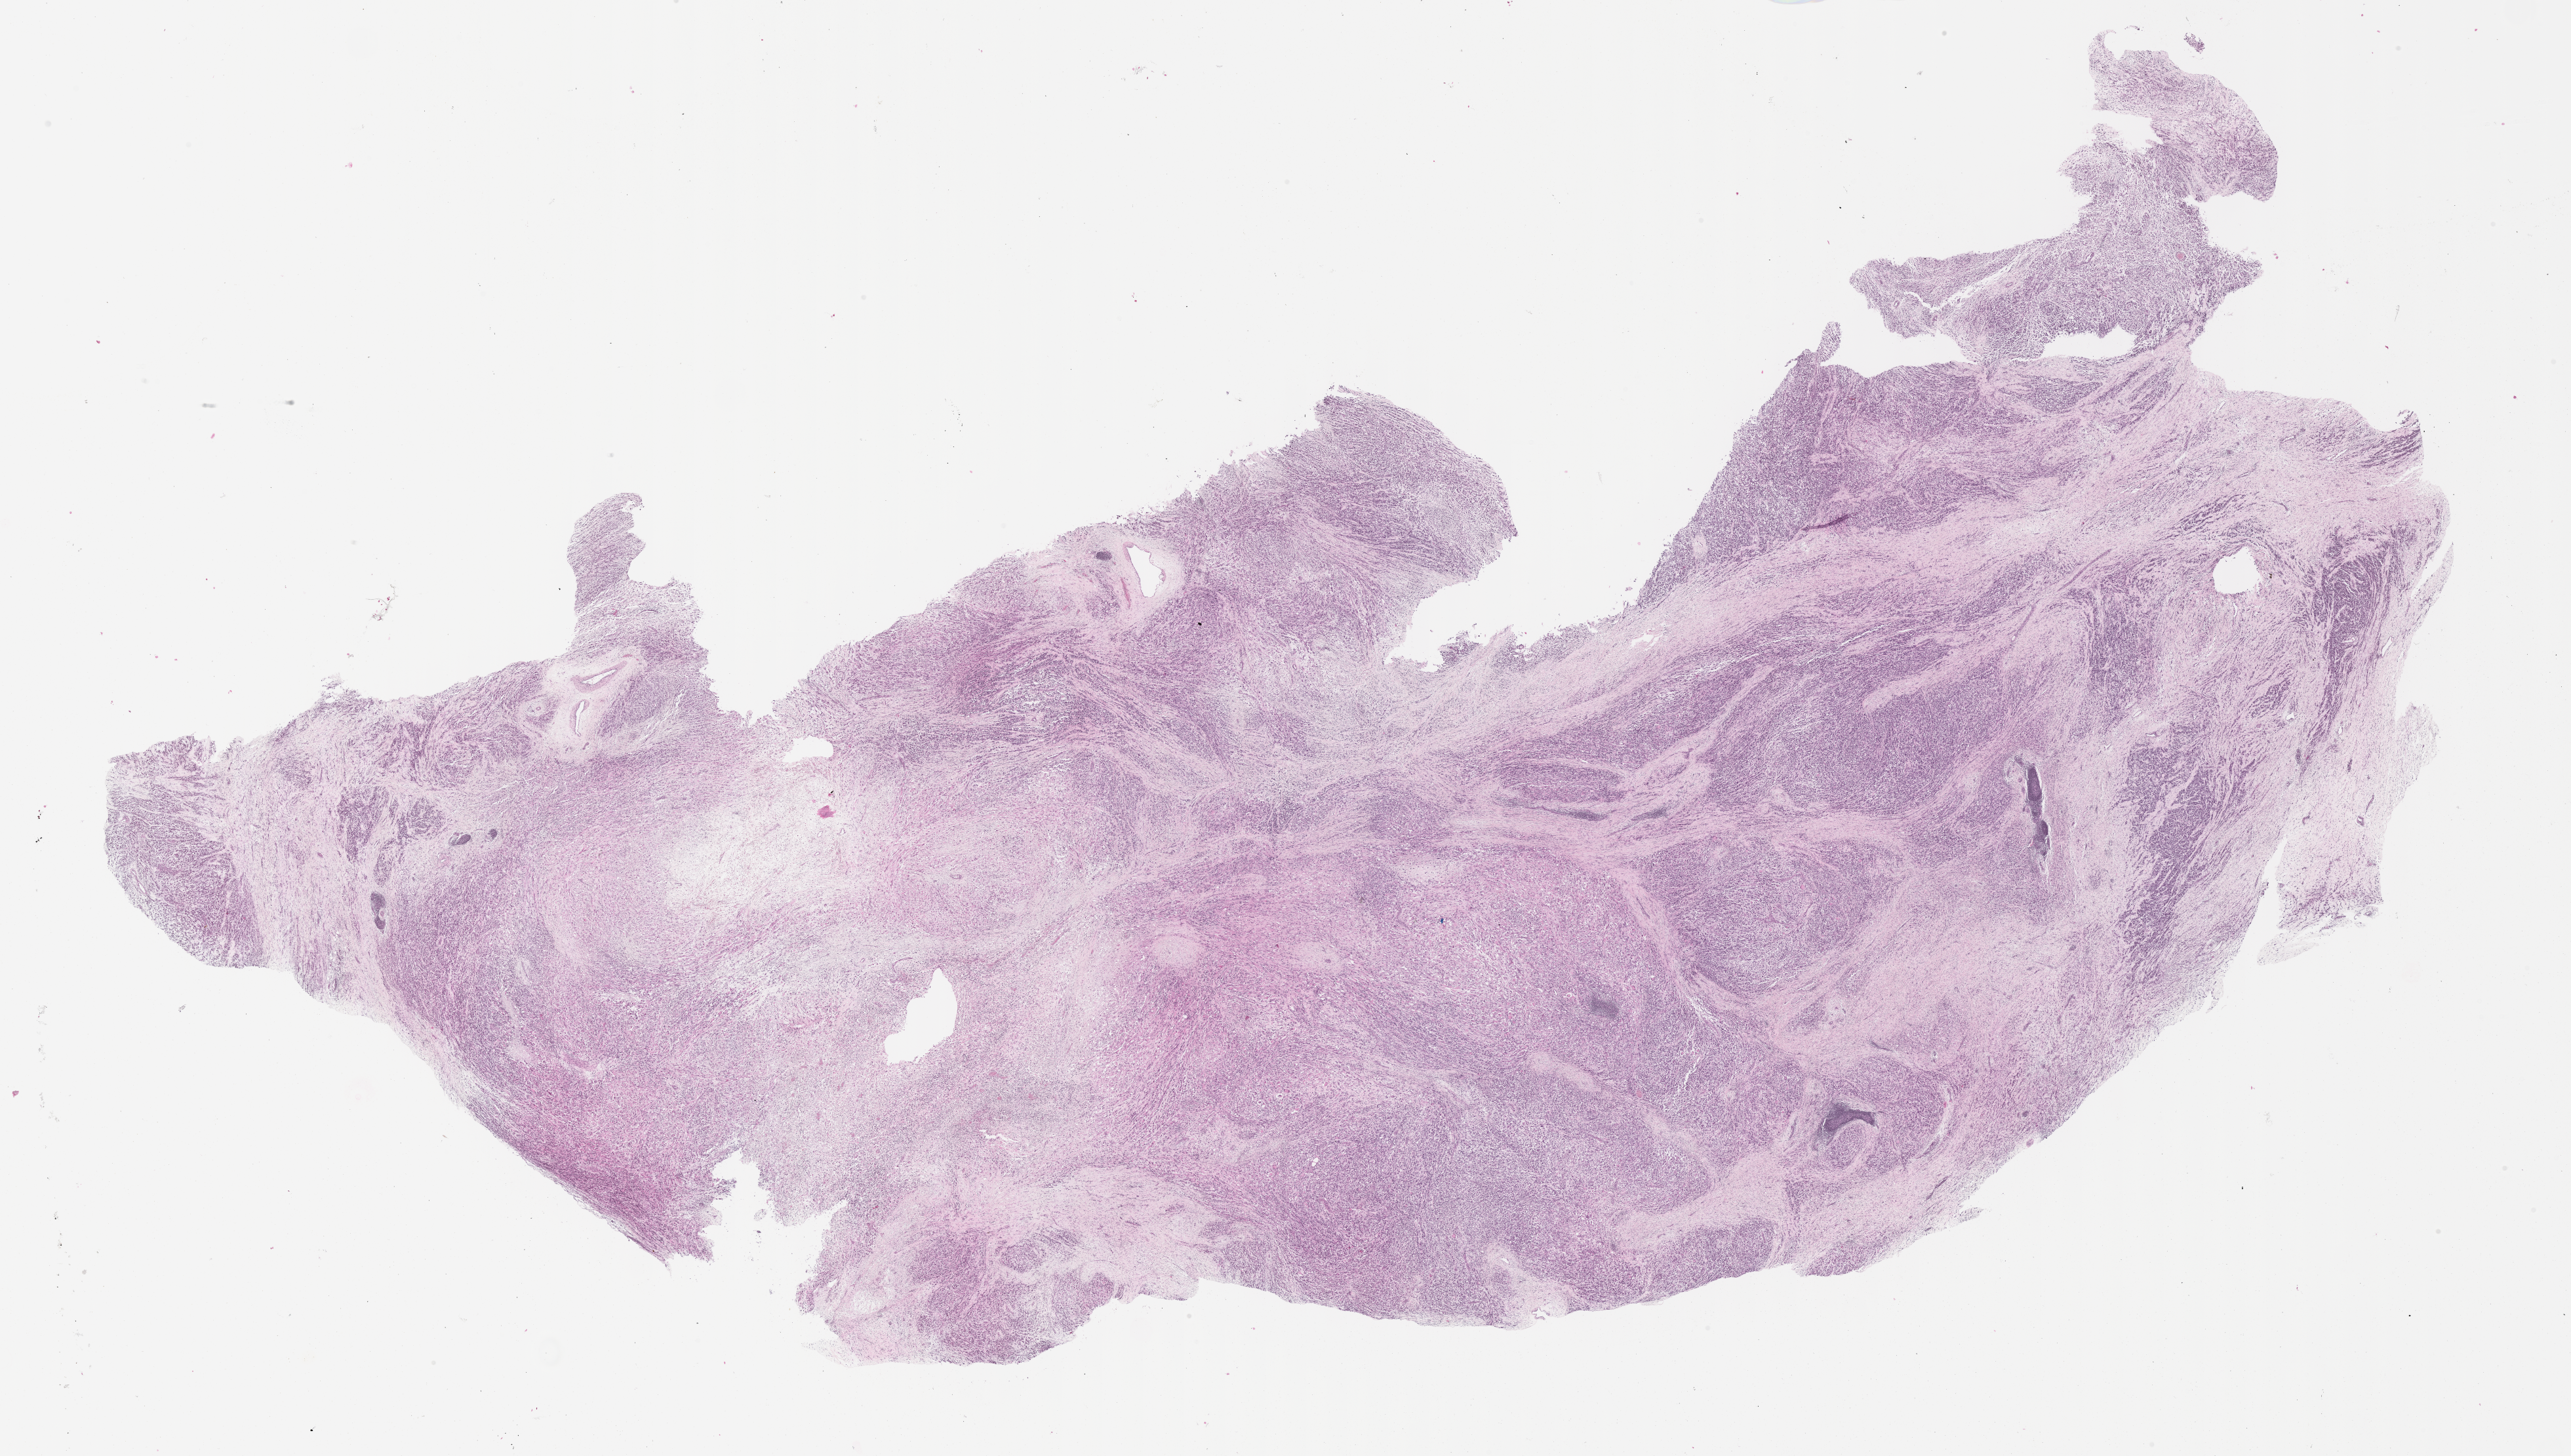
Digitized haematoxylin and eosin-stained section of tumor tissue, whole scanned area (about 31.7 x 18.0 mm) shown as a low-resolution overview. FFPE section. Male patient, age at diagnosis 16.2 years.
Diagnosis: rhabdomyosarcoma; histological classification: embryonal rhabdomyosarcoma.